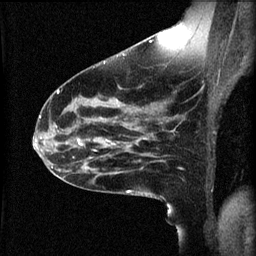
Breast MRI (dynamic contrast-enhanced), one sagittal slice; slice 32 of 60 in the series (ordered by position); 3 images stored at this slice position (order not interpretable as contrast timing); 1.5 T; TE 4.2 ms, TR 8.2 ms; 2 mm slice thickness; 256 × 256 image matrix. Patient: female, 49 years.
Annotated regions visible in this slice (semi-automatic segmentation, software-assisted and operator-edited):
- analysis volume of interest (the breast-tissue region the enhancement analysis was run in; not a lesion): box from (x=66, y=124) to (x=113, y=159) px
- tumour enhancement mask (voxels above the 70 % enhancement threshold inside the analysis volume of interest): (x=78, y=140)–(x=95, y=145)